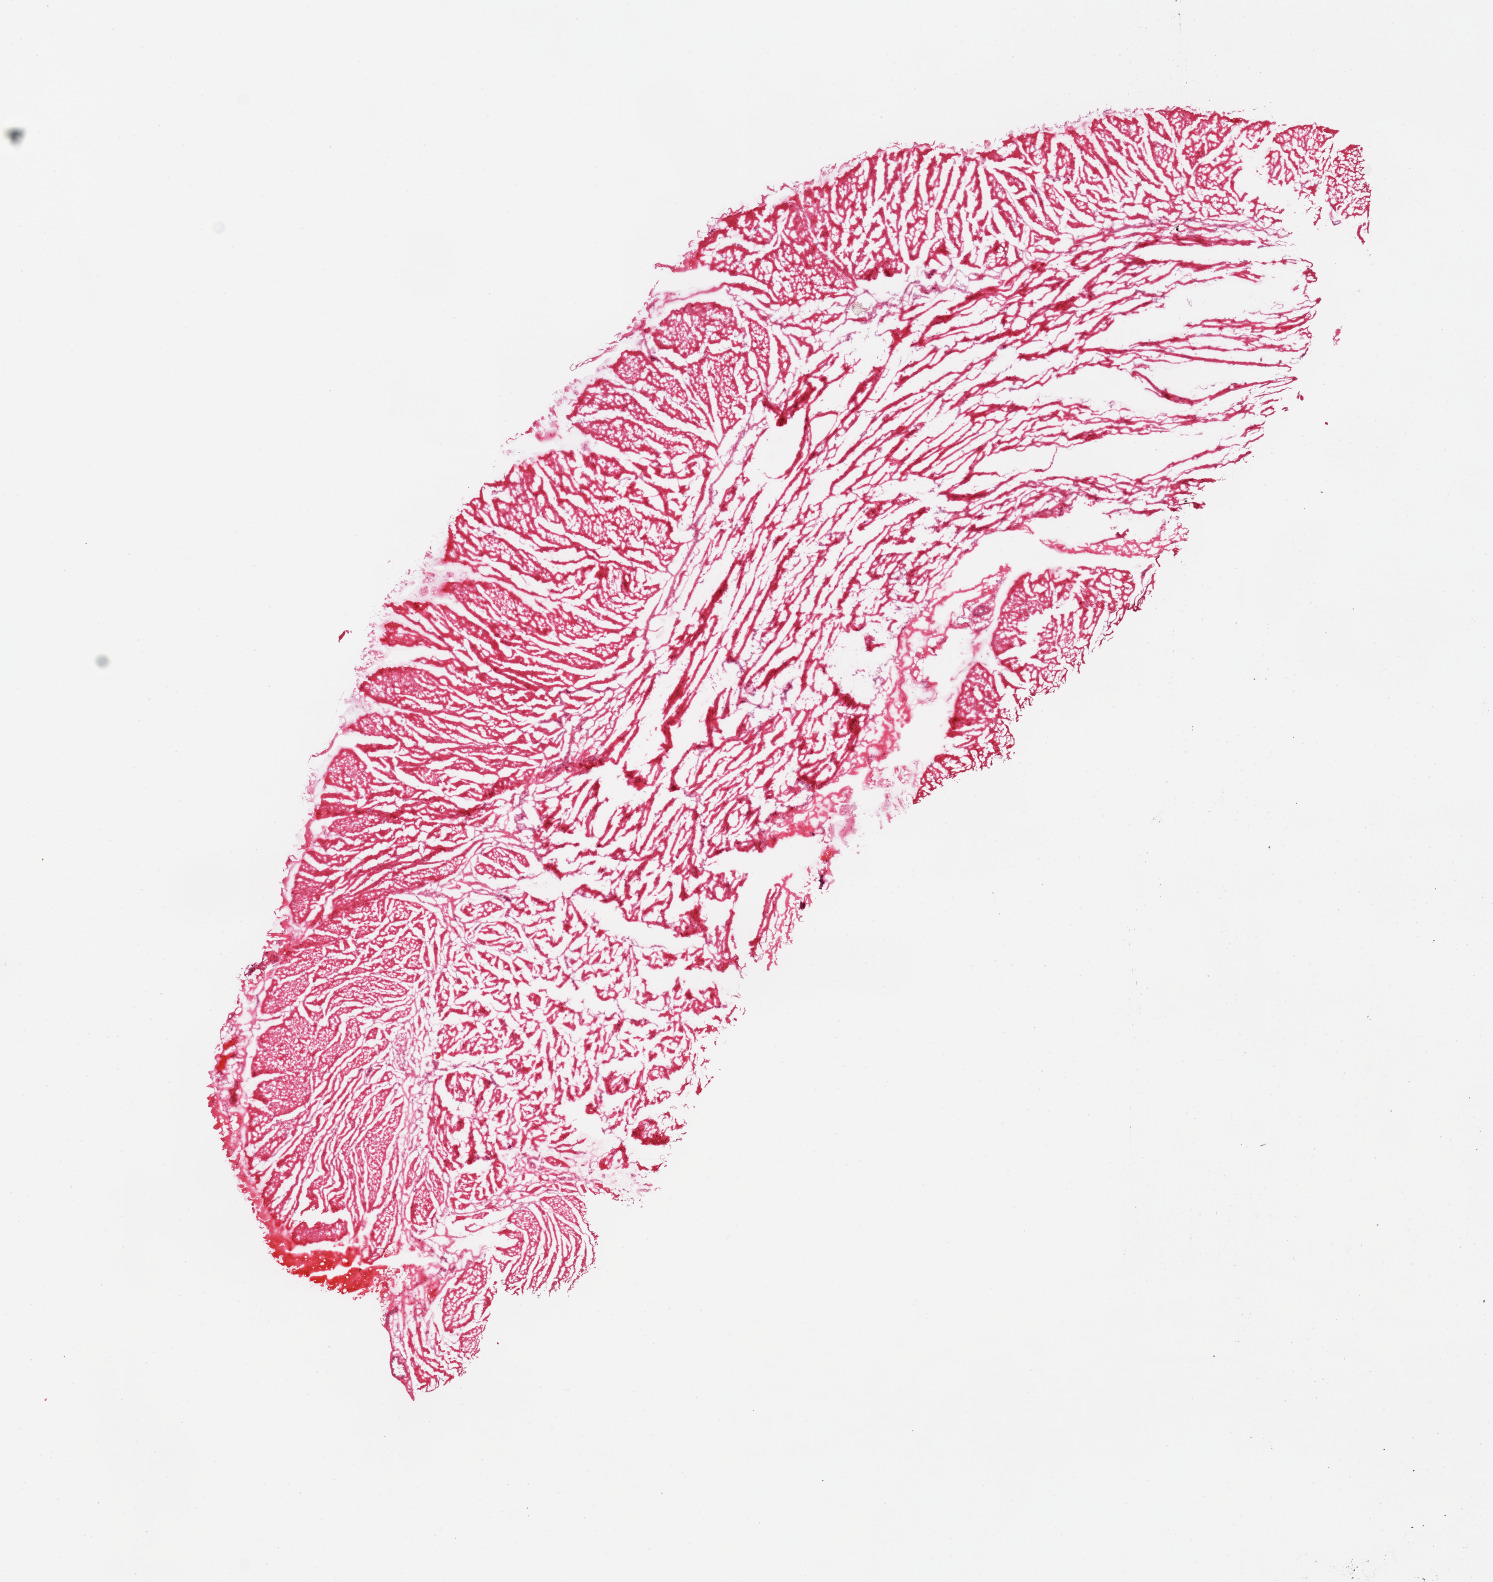
Hematoxylin and eosin (H&E) whole-slide image, low-resolution overview of the scanned area, about 11.8 x 12.5 mm. Frozen section (dry ice). Target tissue: esophageal muscle. Donor tissue sample. Donor: female.
• pathologist's review note for this sample: 1 piece